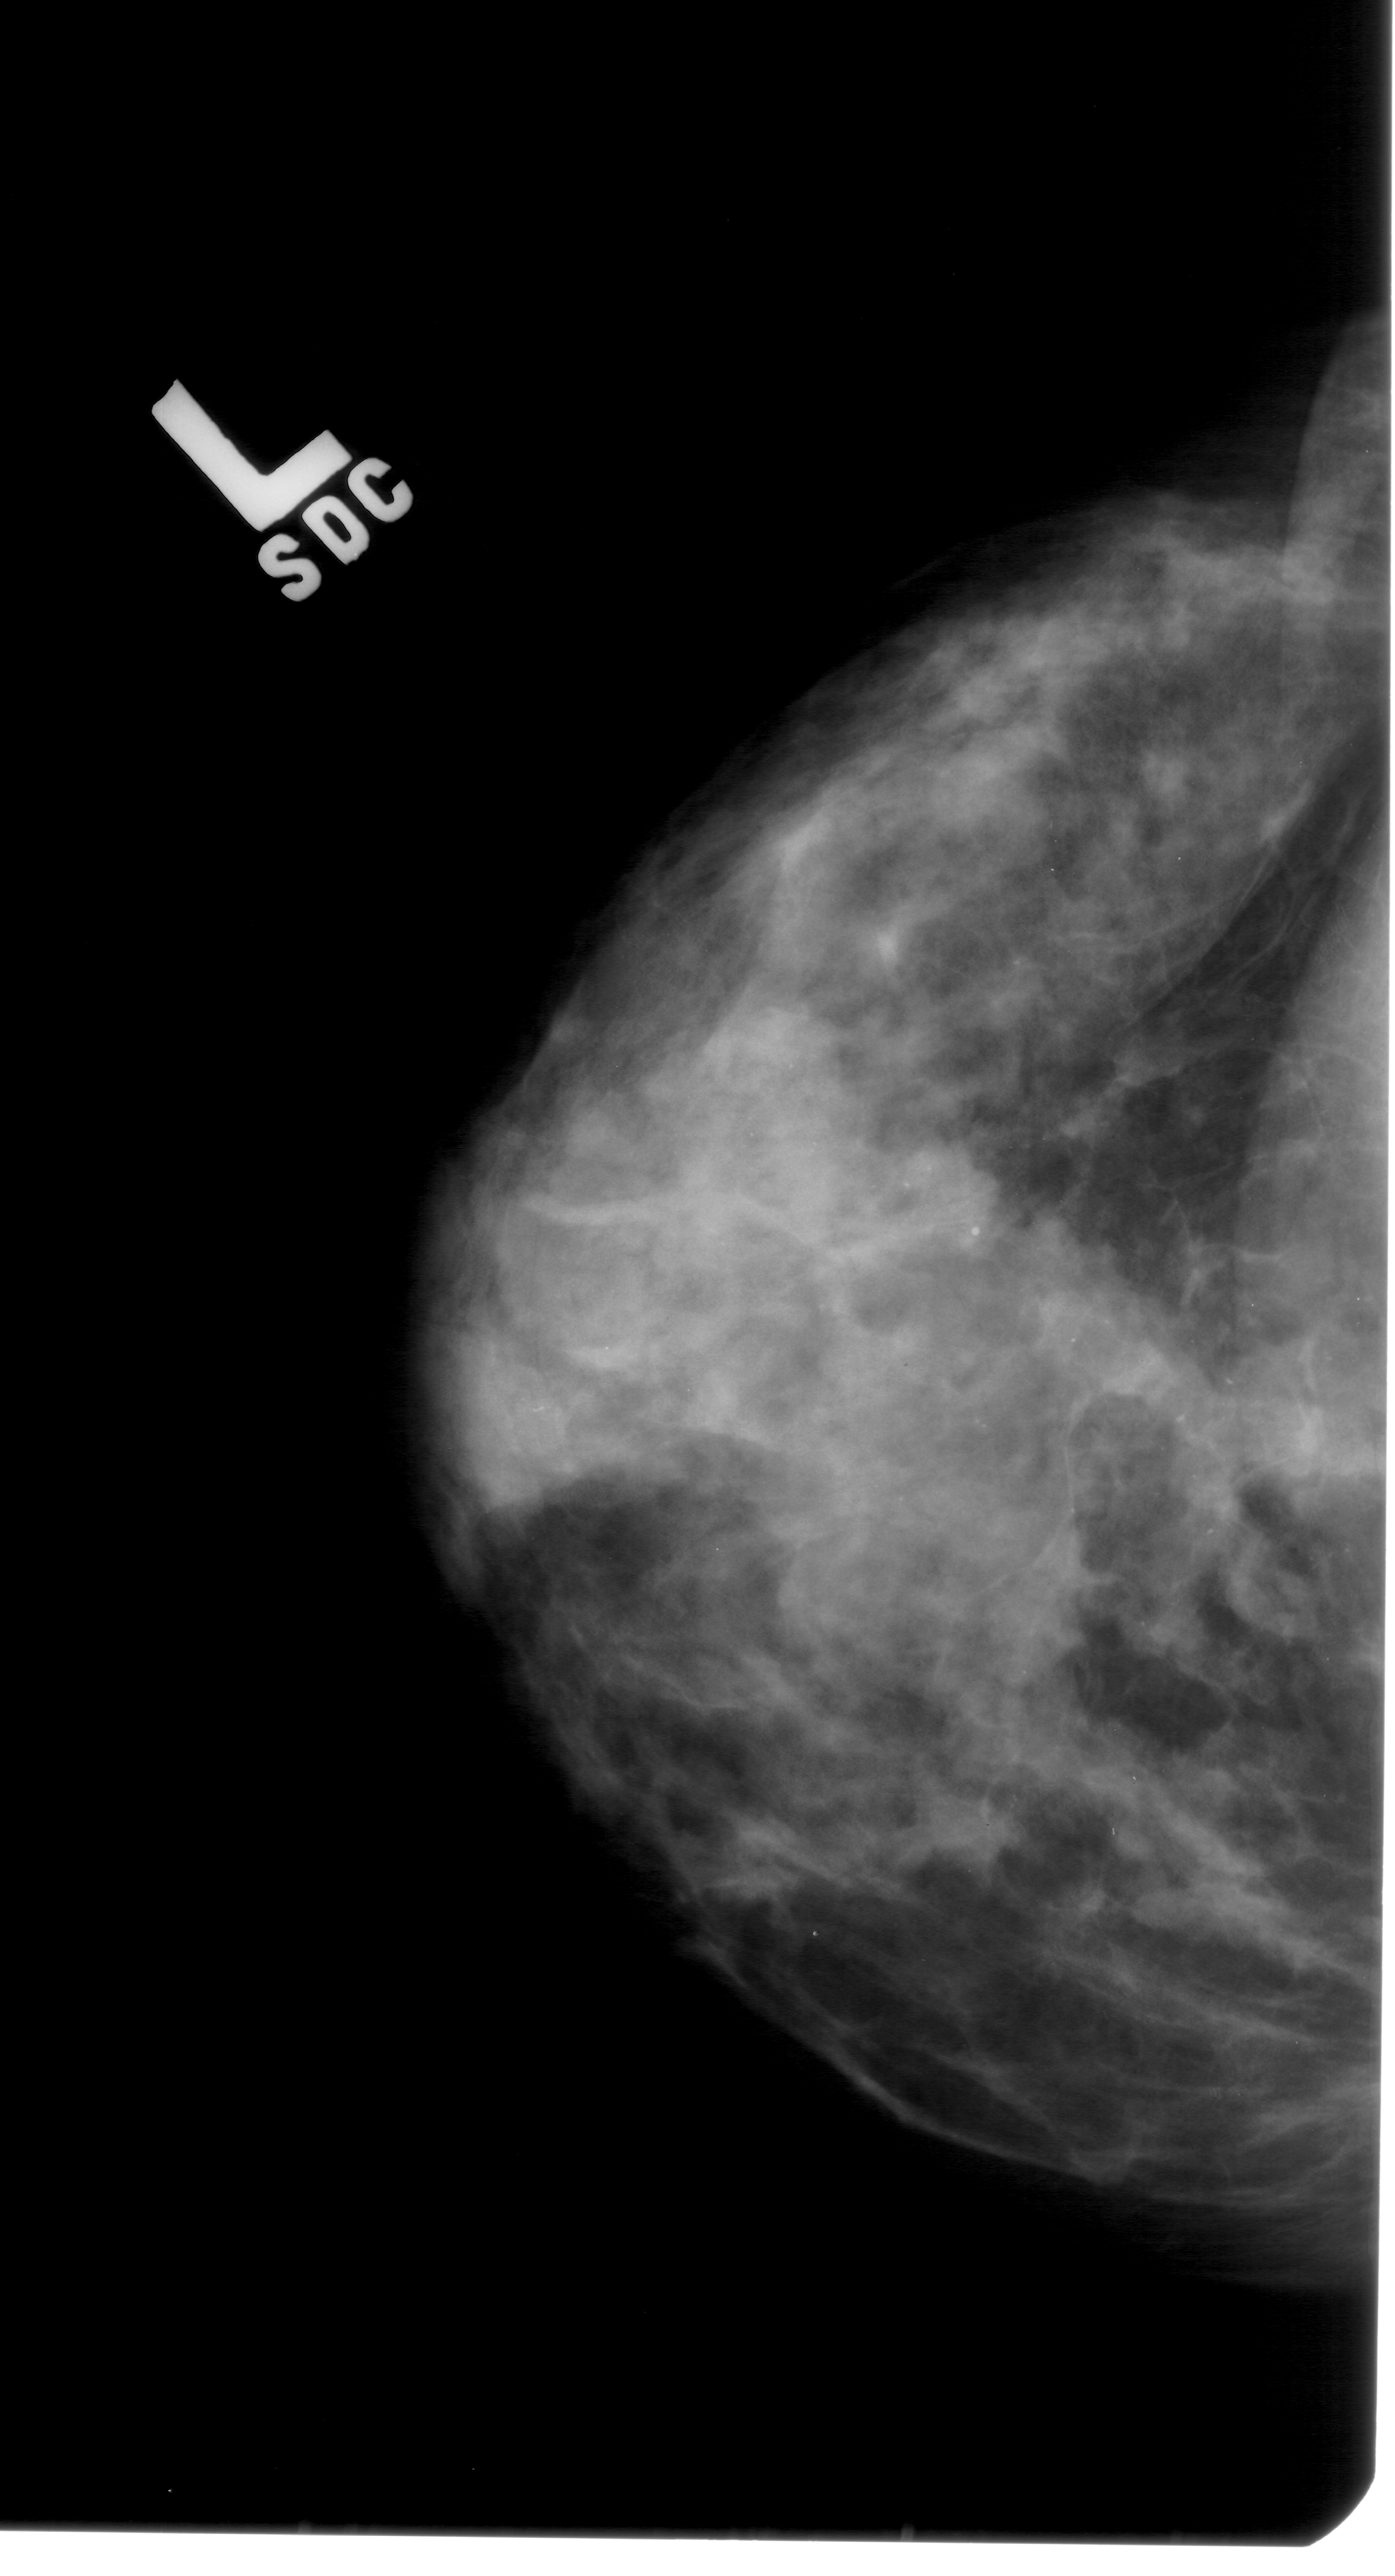
Mammogram (digitized film); left breast; CC view; BI-RADS breast density category 3 (scale 1–4); 1395 × 2576 image matrix.
Marked abnormalities (boxes around the expert regions of interest):
- calcifications, morphology pleomorphic, distribution segmental; BI-RADS assessment category 4; subtlety rating 3 on a 1 (subtle) to 5 (obvious) scale; pathology (as recorded): malignant: box from (x=496, y=1010) to (x=1379, y=1664) px